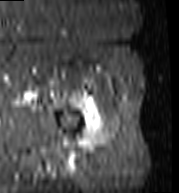
MRI of an extremity soft-tissue mass, one axial slice; position 95 of 103 along the scan axis; STIR; MR volume resampled by the dataset authors to the PET/CT grid (not the native acquisition matrix); 179 × 193 image matrix, field of view 175 × 188 mm. Female patient. Case-level facts recorded for this patient, not image findings: histological type: undifferentiated – high grade; grade: high; site of the primary tumour: left thigh.
Outlined on this slice (expert contour drawn on MRI and transferred to this co-registered scan by the dataset authors):
- gross tumour volume including surrounding oedema: bounding box <86,112,106,147> (left, top, right, bottom; pixels)